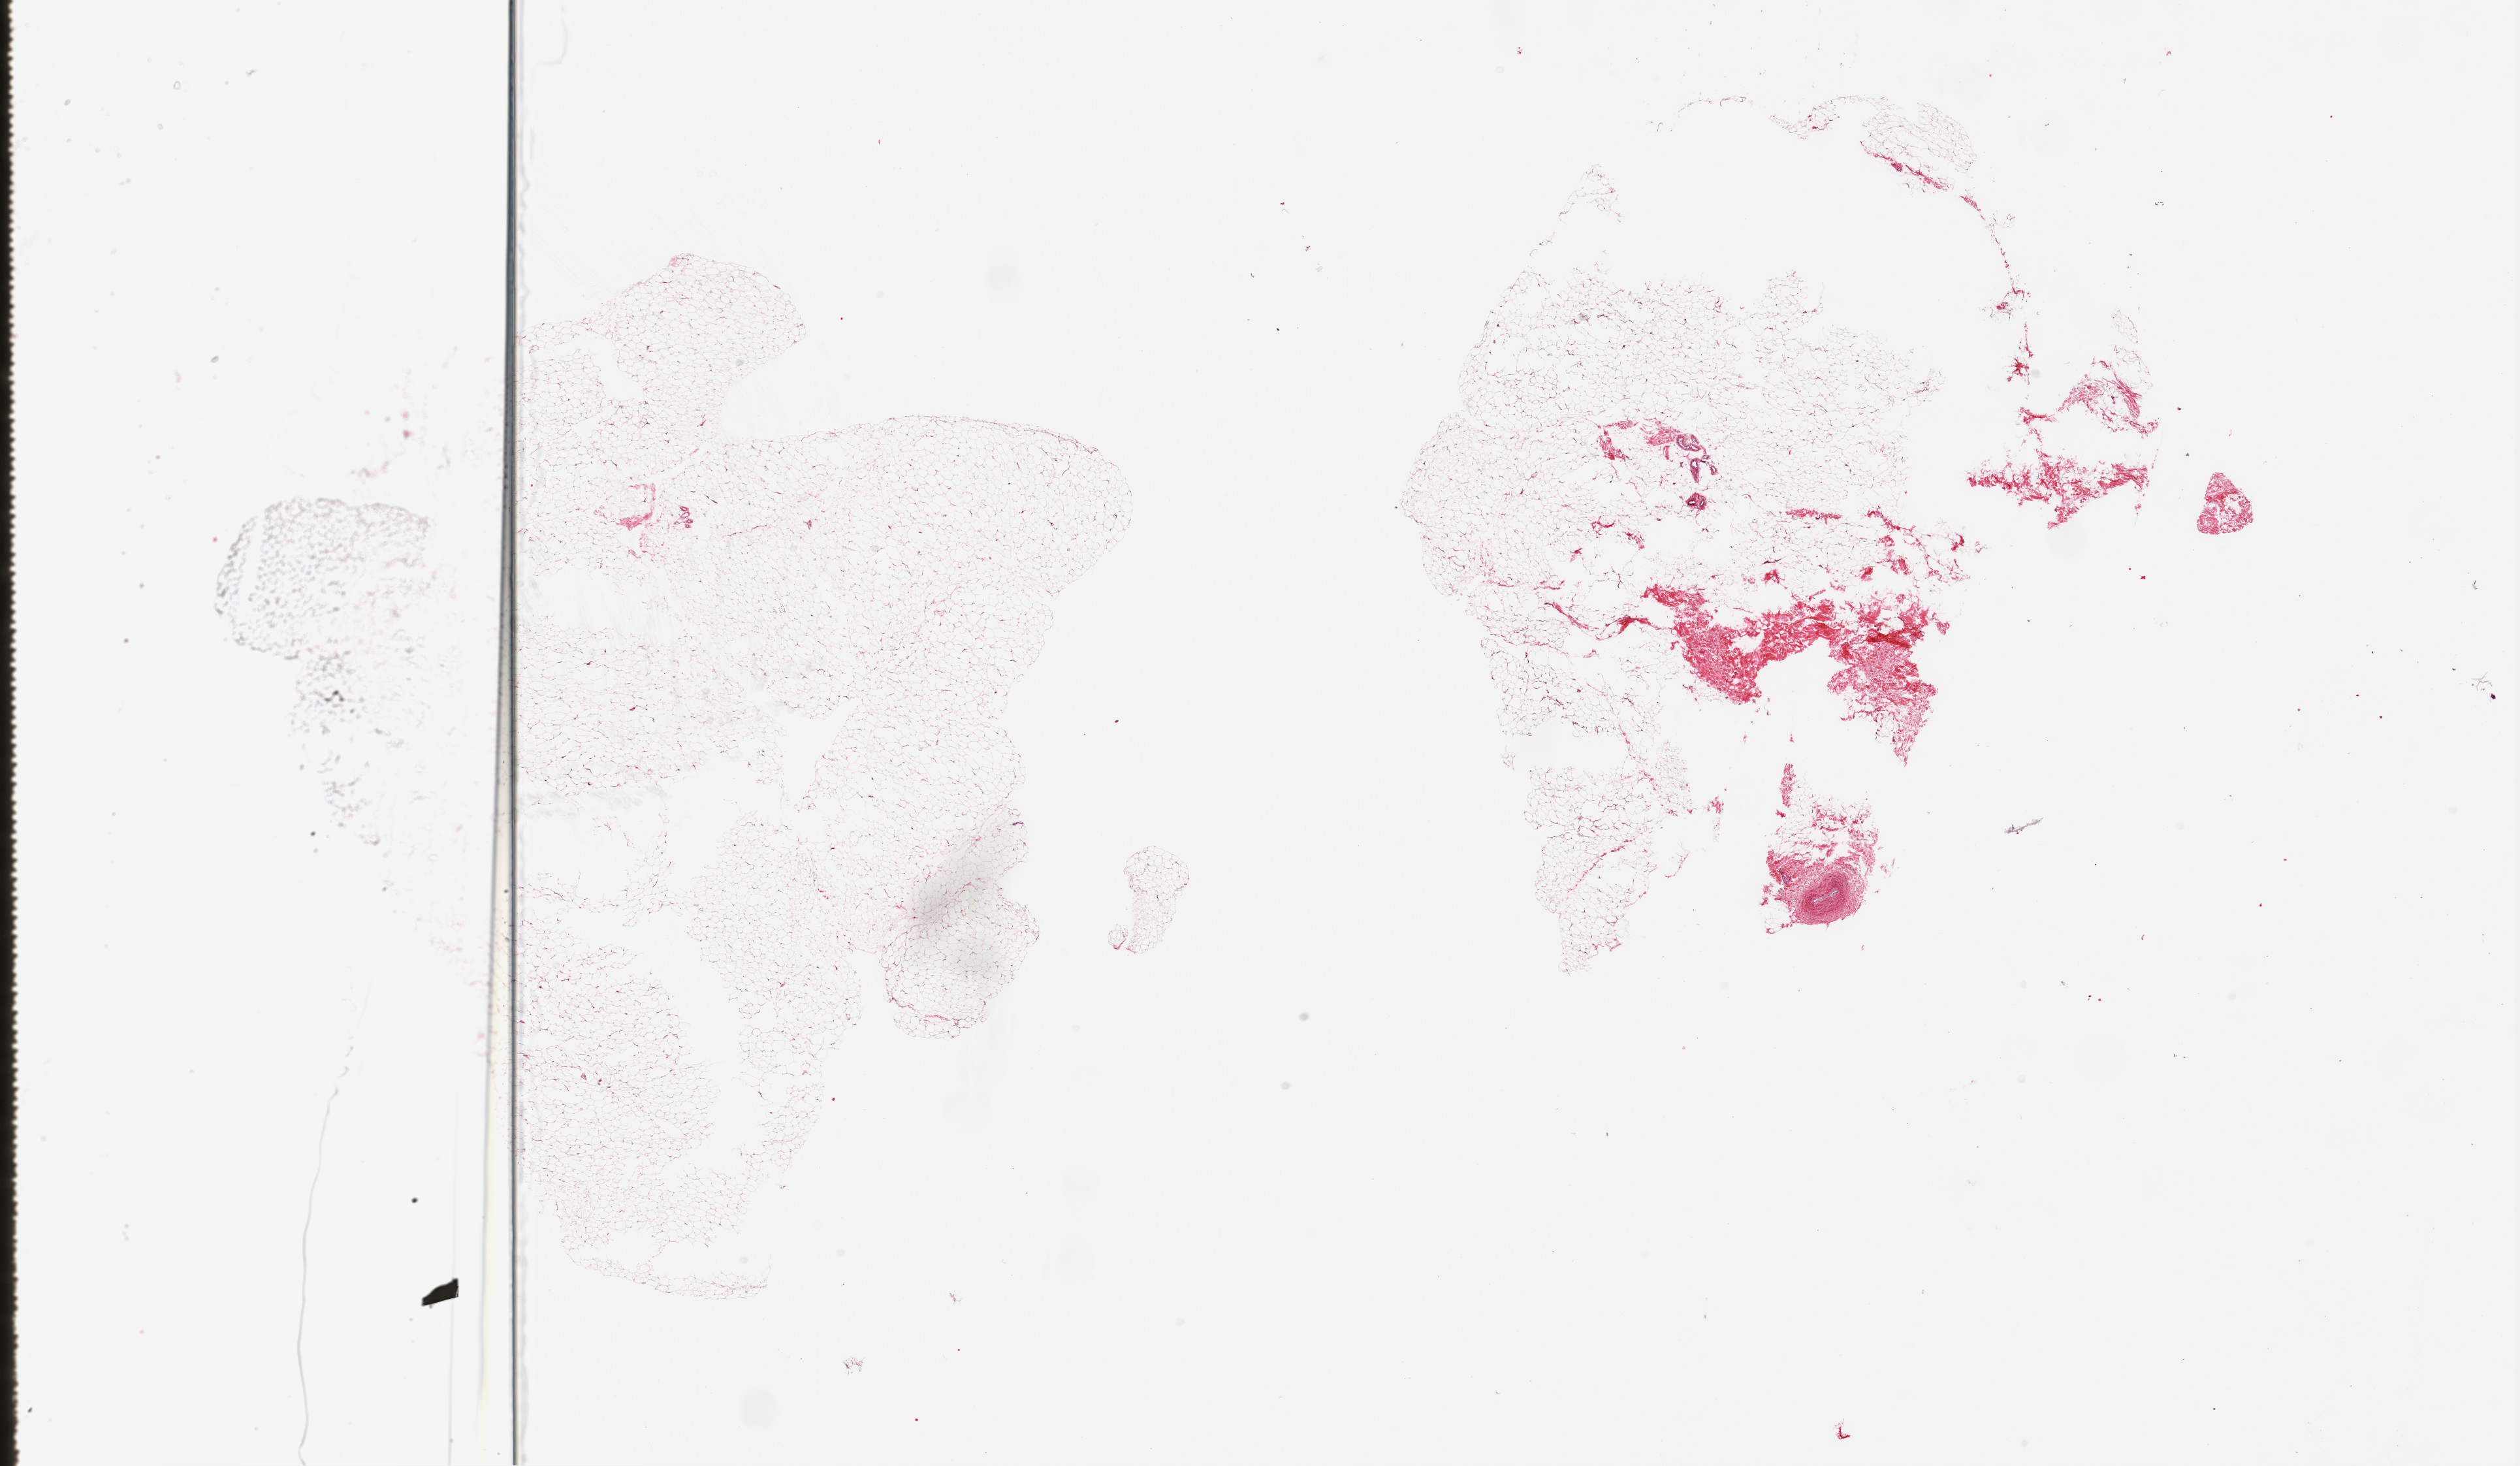
Digitized hematoxylin and eosin (H&E)-stained section — whole scanned area (about 30.5 x 17.8 mm) shown as a low-resolution overview, PAXgene-fixed paraffin-embedded (PFPE) section, target tissue: breast, donor tissue sample. Male donor.
* pathologist's review note for this sample: 2 pieces, fibroadipose elements only